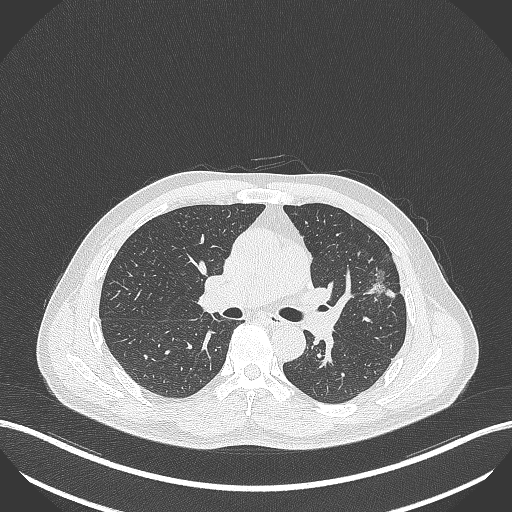
Chest CT, one axial slice. Position 233 of 418 along the scan axis. 120 kVp. Lung window (W 1500 / L -600 HU). 1 mm slice thickness. 512 × 512 image matrix. Patient: male, 55 years. Case-level facts recorded for this patient, not image findings: clinical TNM (as recorded): T1c N0 M0; histopathological grade: G2-3.
Structures marked on this image (bounding box drawn by a radiologist):
- lung tumour (recorded histology: adenocarcinoma): bounding box (x1, y1, x2, y2) in pixels: (362, 263, 397, 301)